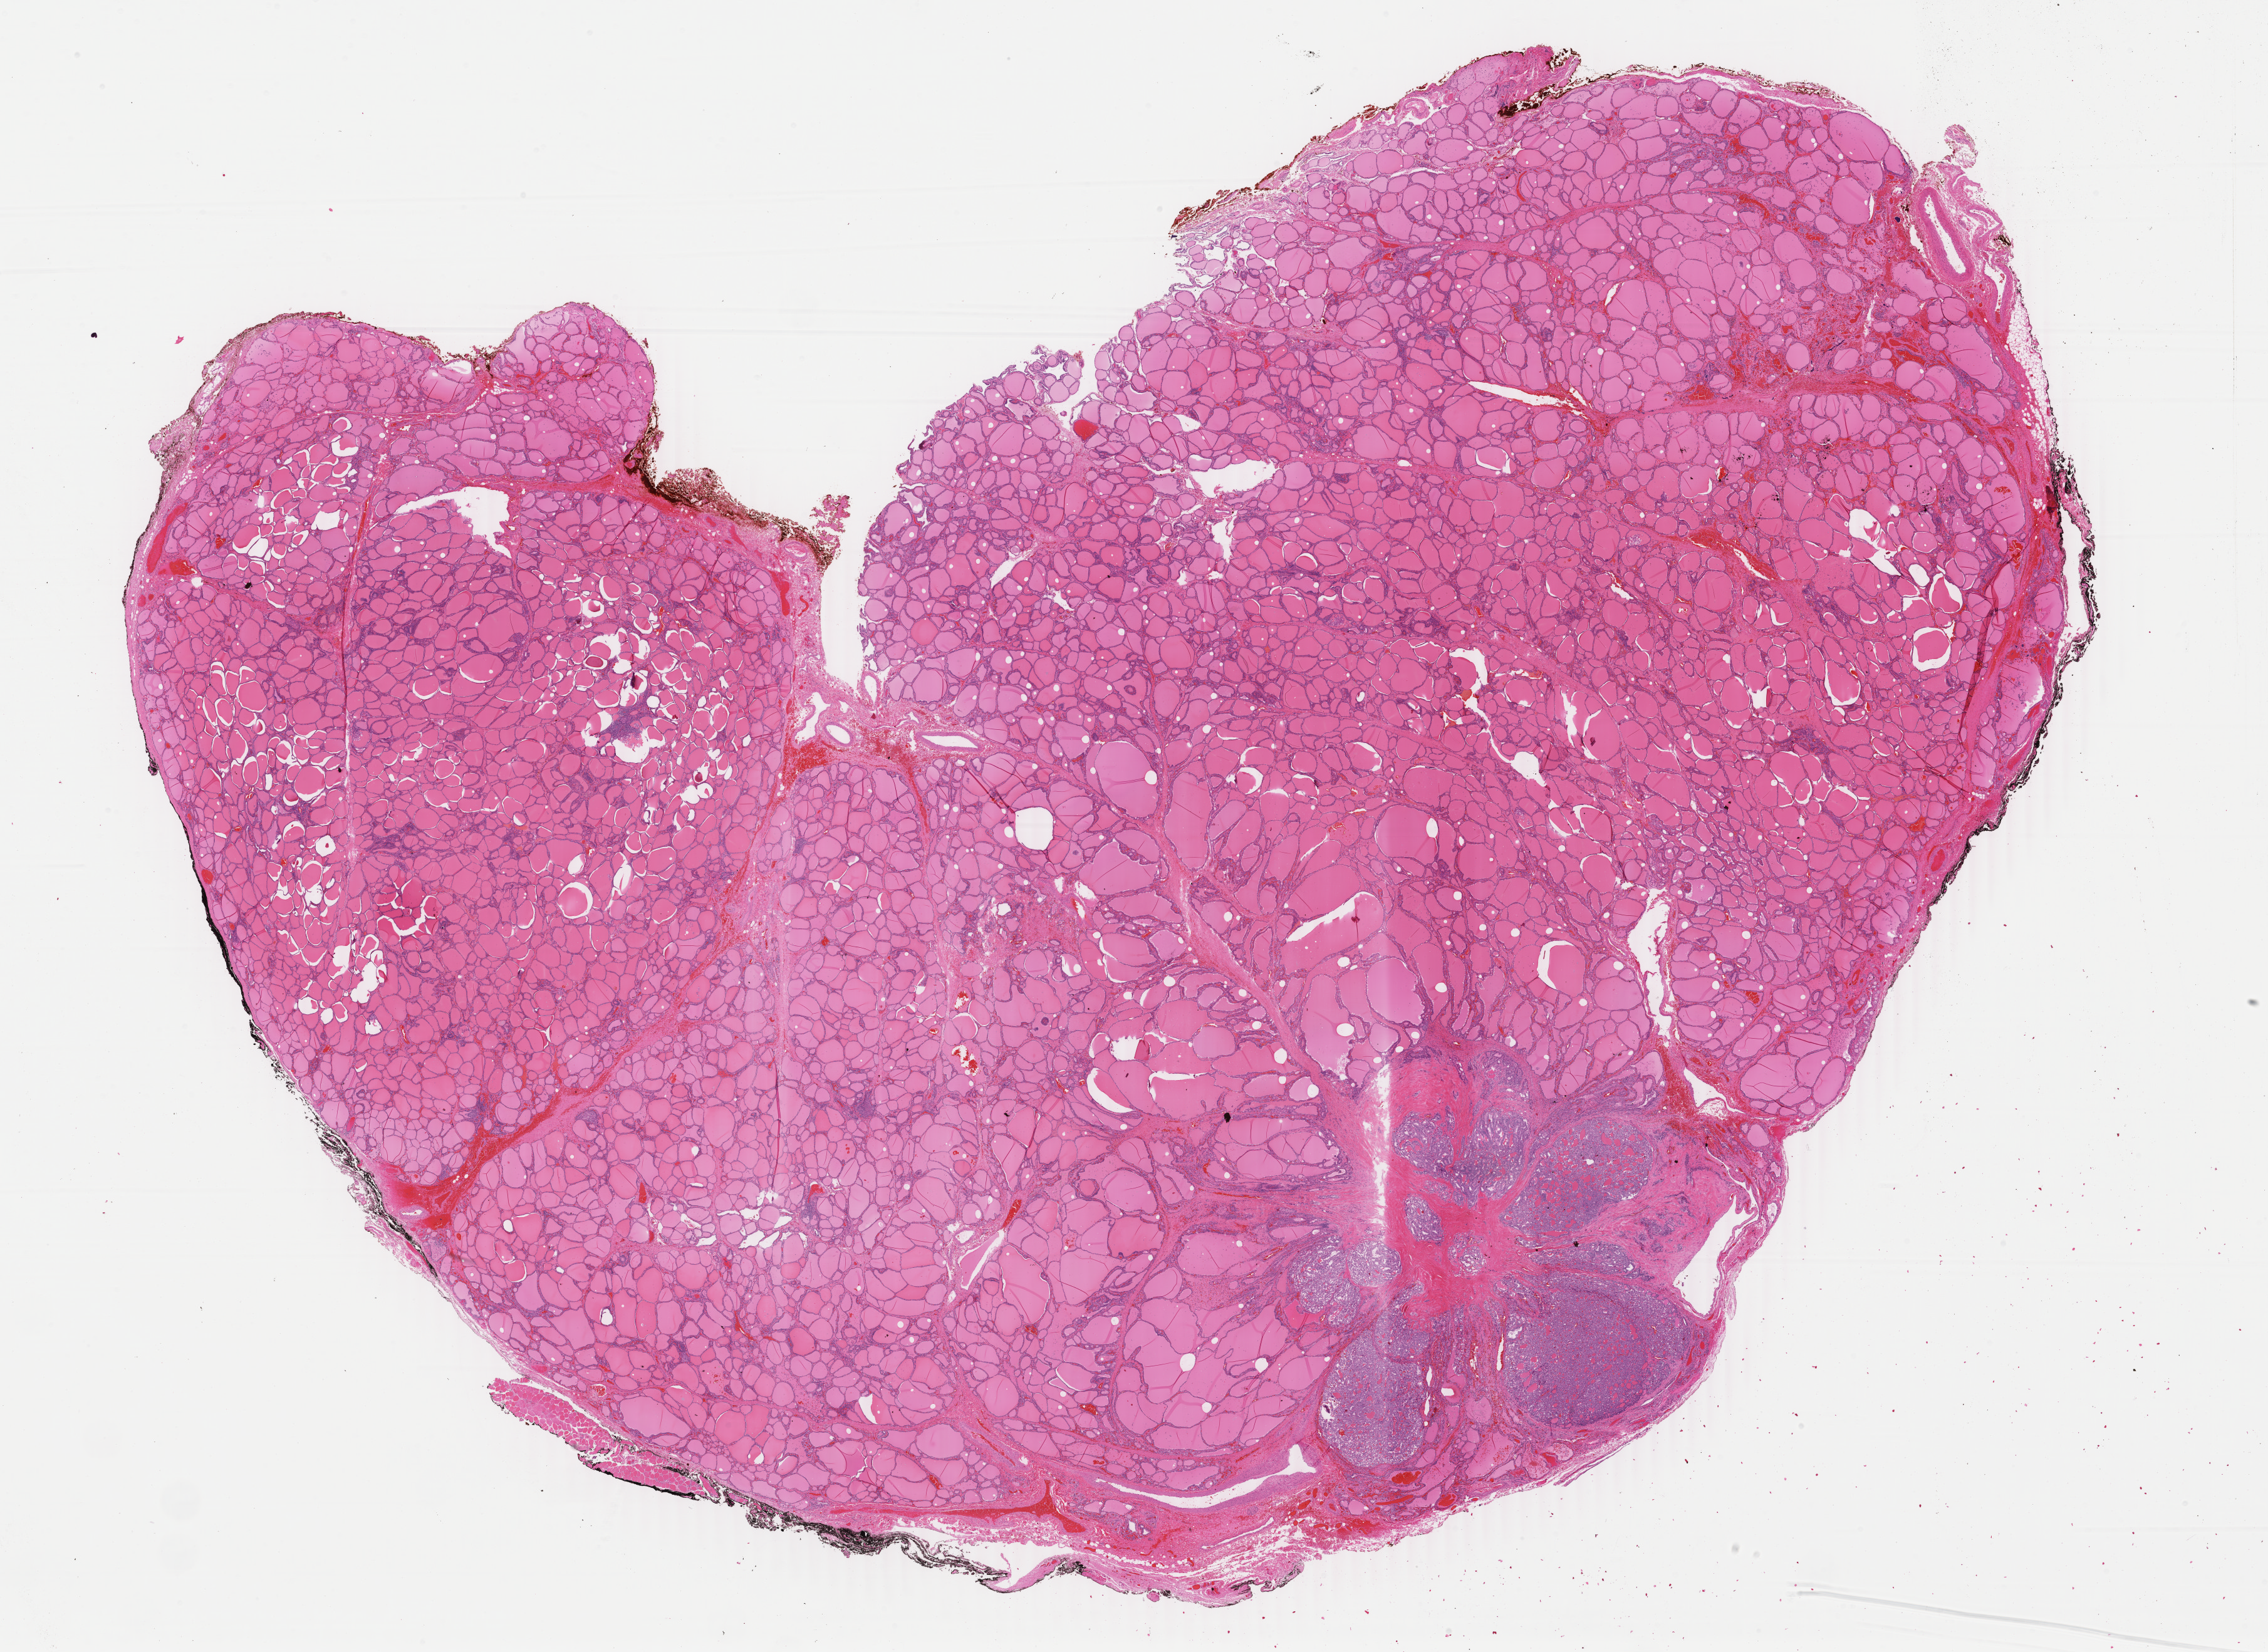
Digitized H&E tissue section (whole slide) — whole scanned area (about 28.8 x 21.0 mm) shown as a low-resolution overview; FFPE section; sample: primary tumour, thyroid. Female, age 24 years at initial diagnosis.
- laterality: left
- histologic diagnosis: Papillary adenocarcinoma, NOS (thyroid gland)
- AJCC pathologic stage: I (6th edition)
- lymph nodes positive (case pathology): 0 of 3 examined